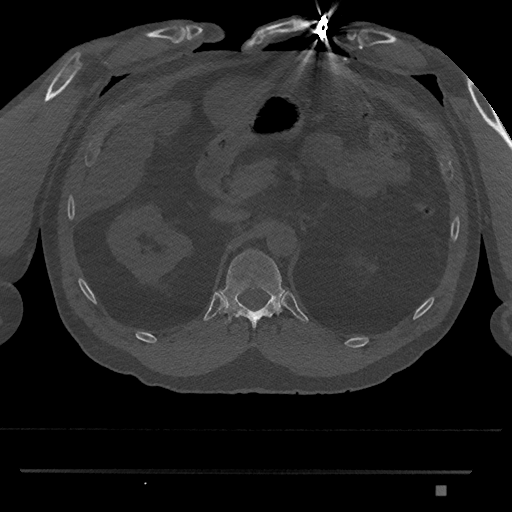
CT including the spine, one axial slice. Slice 887 of 1134 in the series (ordered by position). Reconstruction kernel Br40s/3. 120 kVp. Bone window (W 1800 / L 400 HU). 0.5 mm slice thickness. 512 × 512 image matrix, field of view 429 × 429 mm. Male patient, age 65 years. Case-level facts recorded for this patient, not image findings: primary cancer: prostate.
Outlined on this slice (semi-automatic segmentation, software-assisted and operator-edited):
- T12 vertebra: box from (x=219, y=249) to (x=286, y=330) px